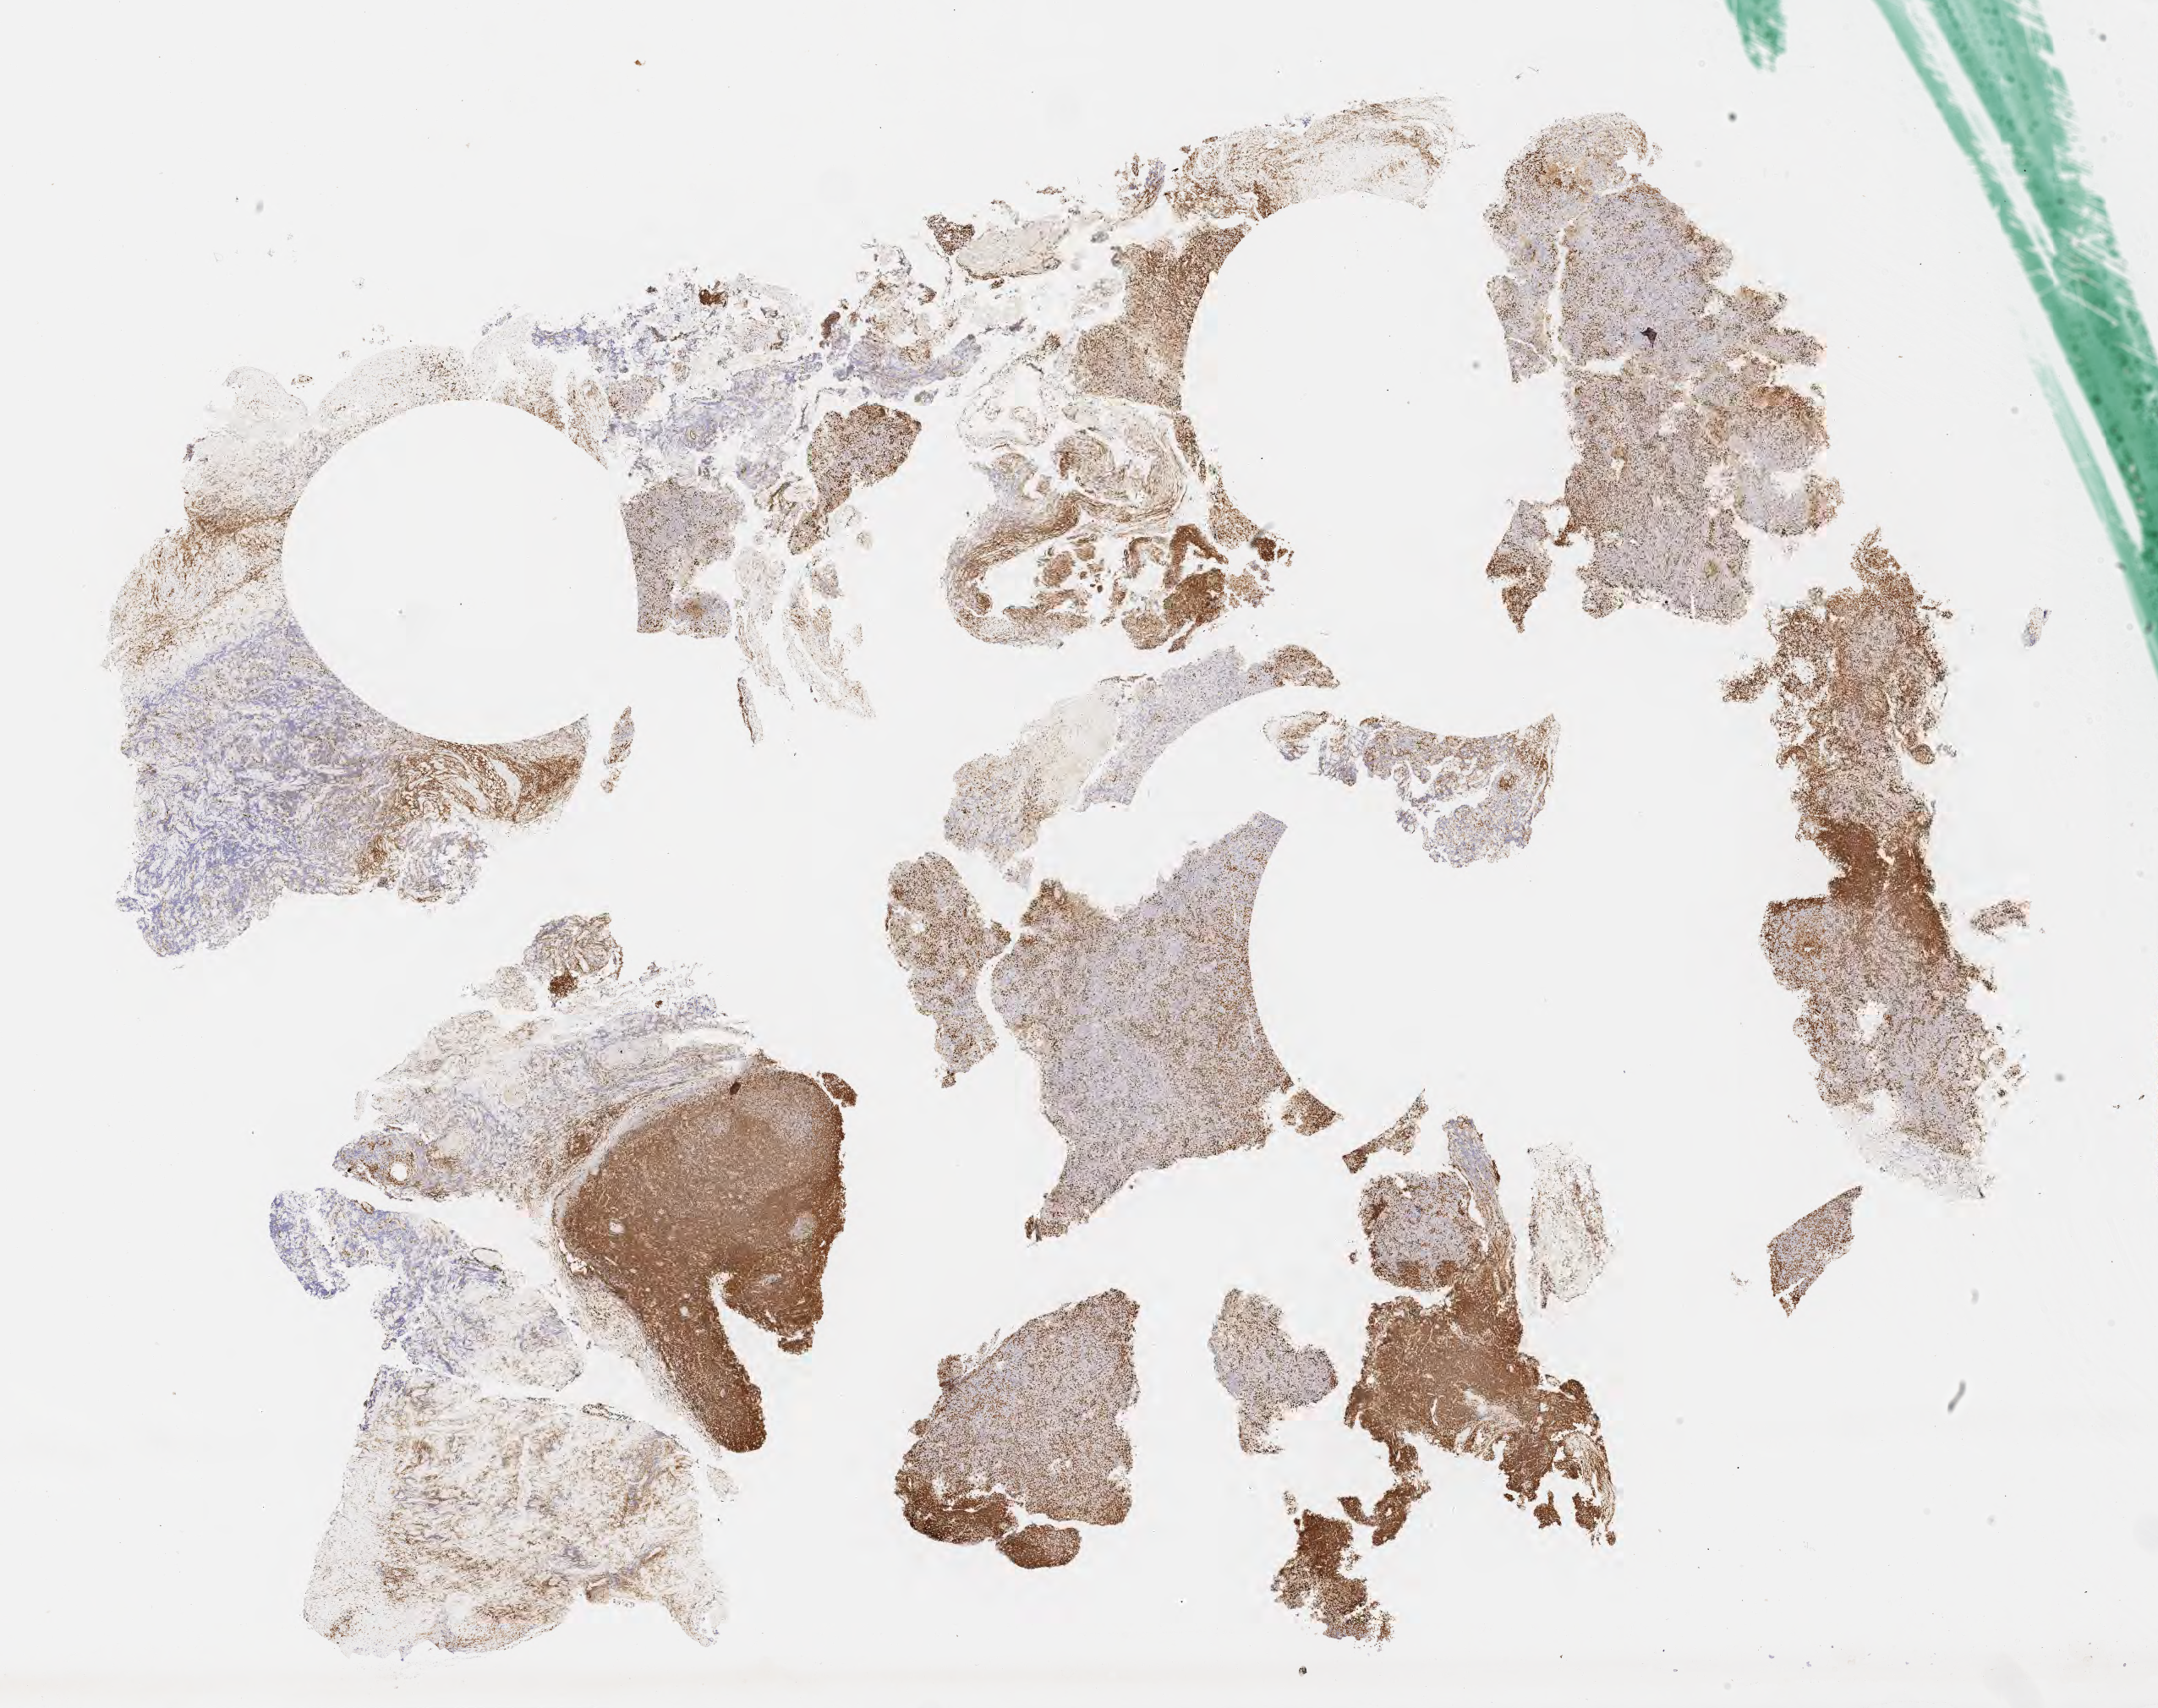
IHC for CD3, whole-slide image, low-resolution overview of the scanned area, about 20.6 x 16.3 mm, specimen: tumor tissue, site: lymph node. Male patient, aged 29.
Histologic diagnosis: Diffuse large B-cell lymphoma, NOS.